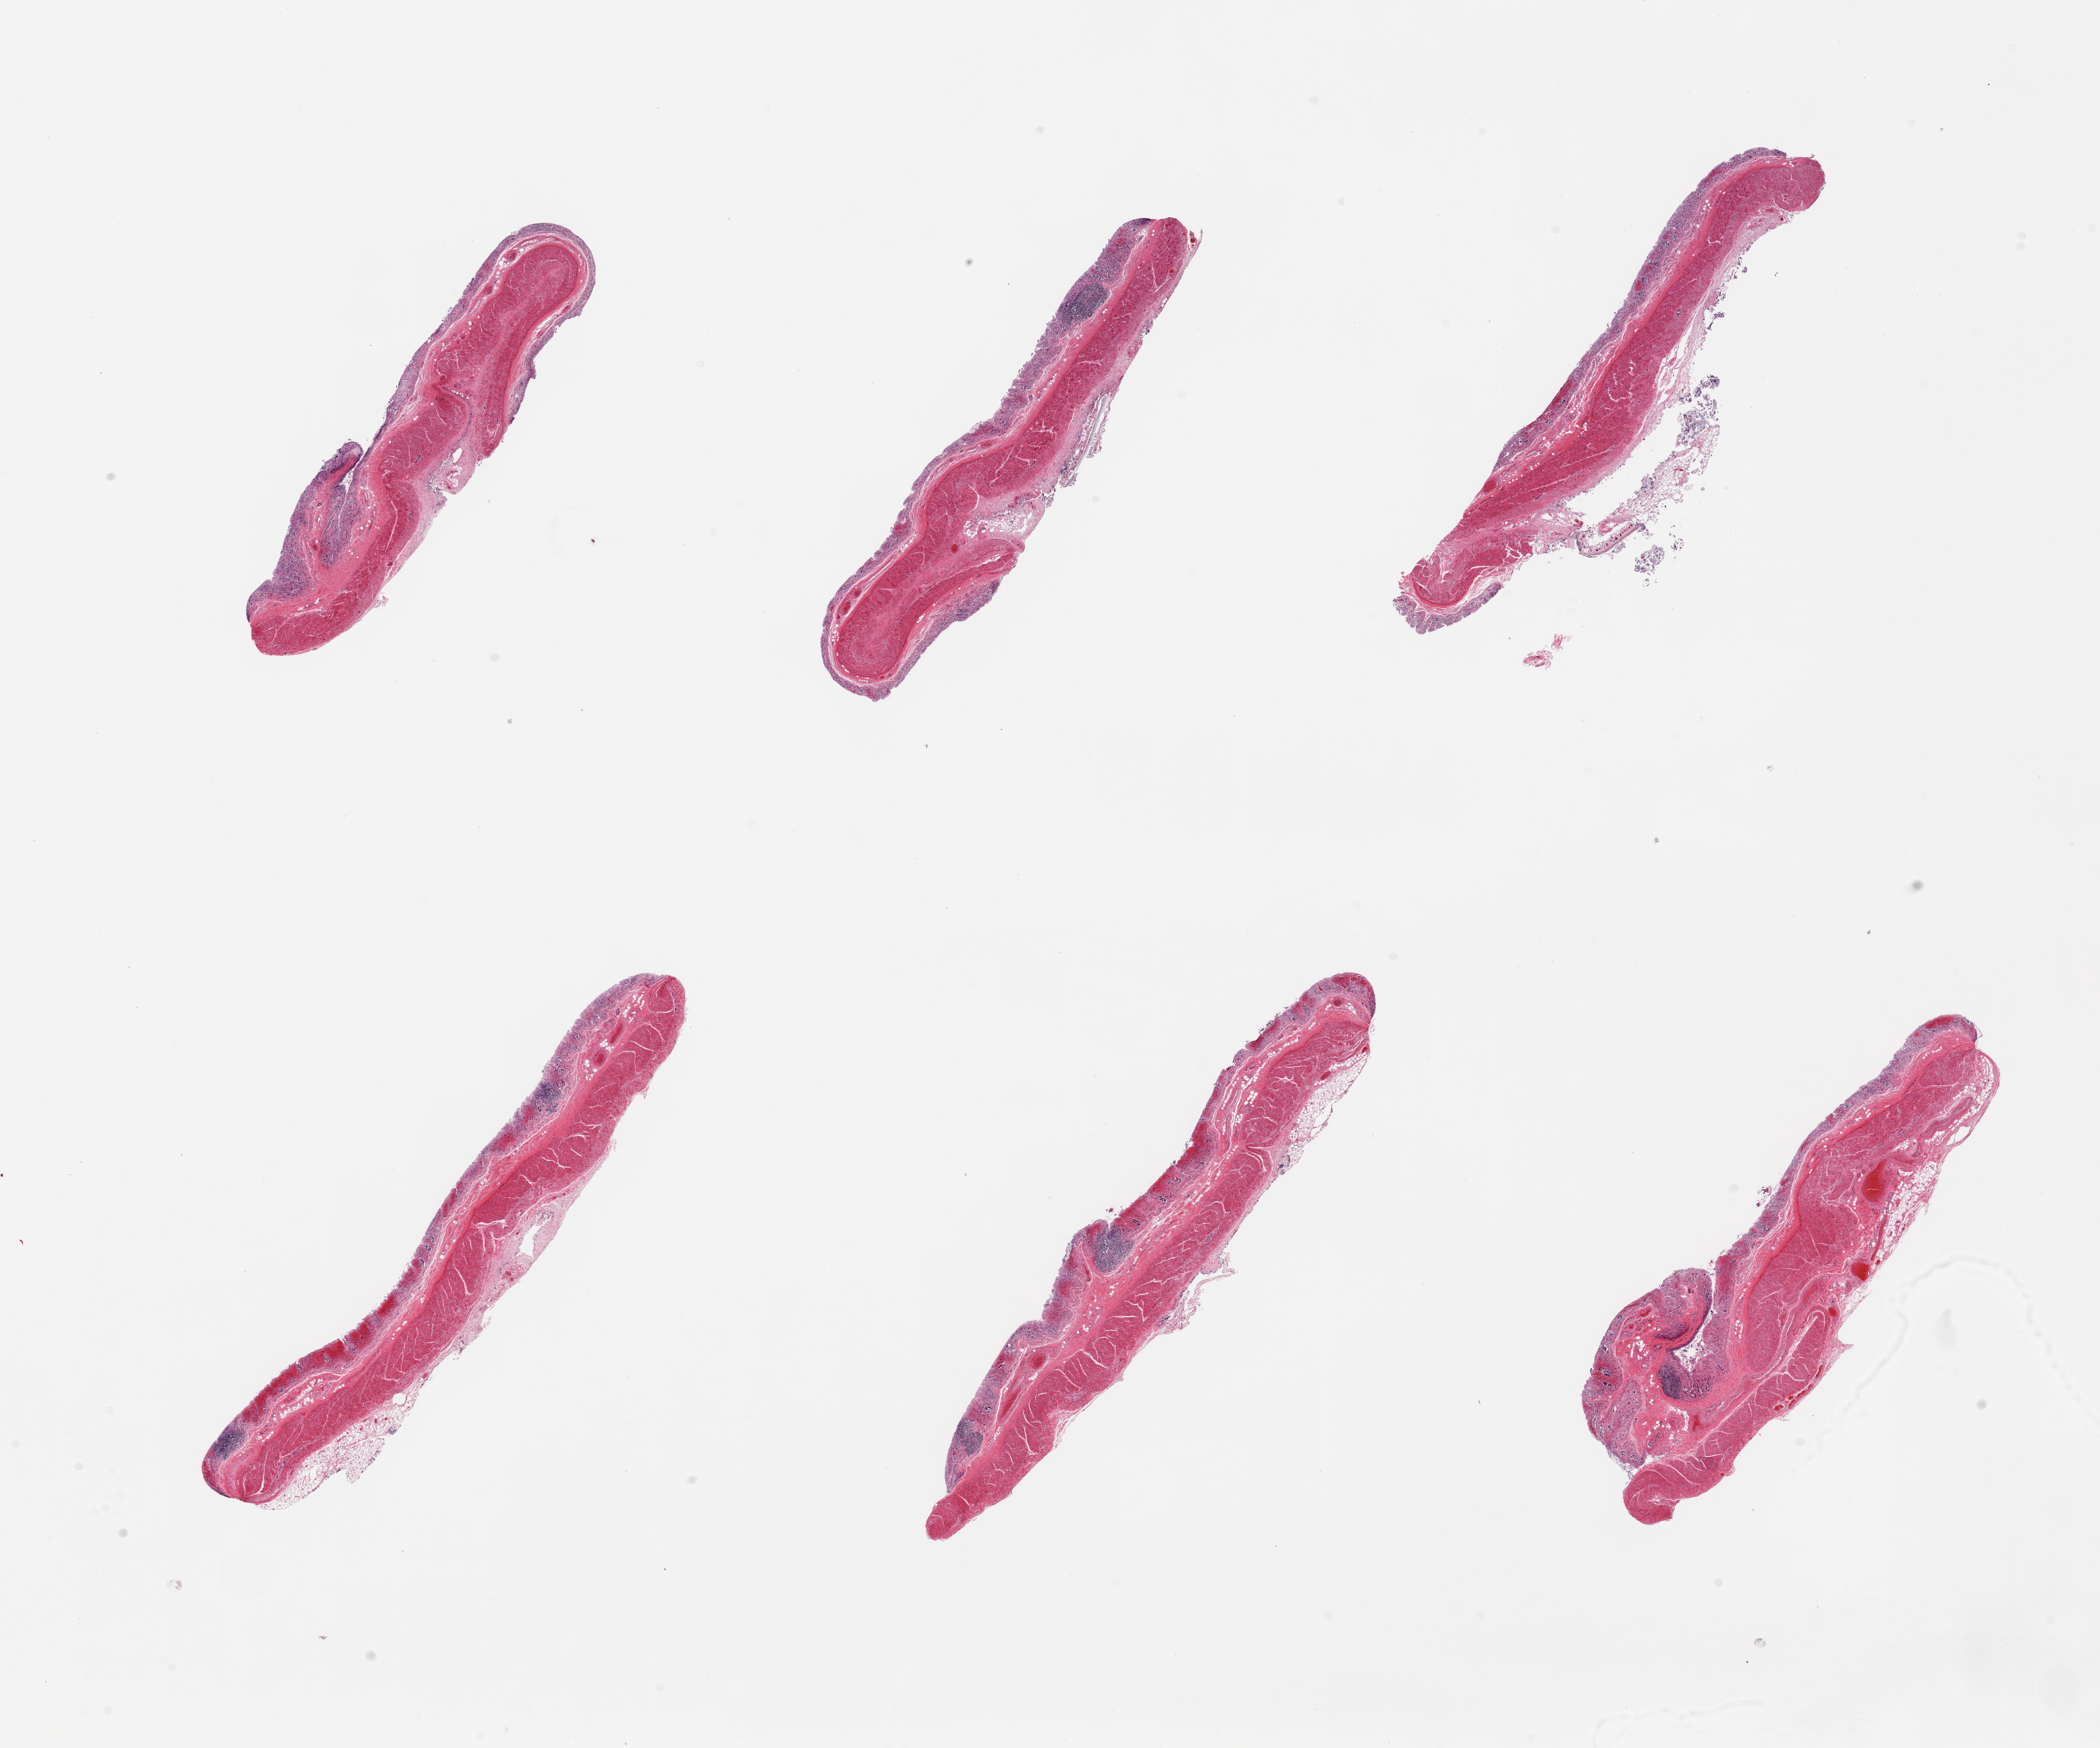
Whole-slide image, hematoxylin and eosin (H&E) stain, a low-resolution overview of the entire scanned area, about 24.6 x 20.5 mm. PAXgene-fixed paraffin-embedded (PFPE) section. Section of transverse colon (target tissue). Tissue donor sample. Donor sex: male.
Pathologist's review note for this sample: 6 pieces; mucosa autolyzed muscle intact.